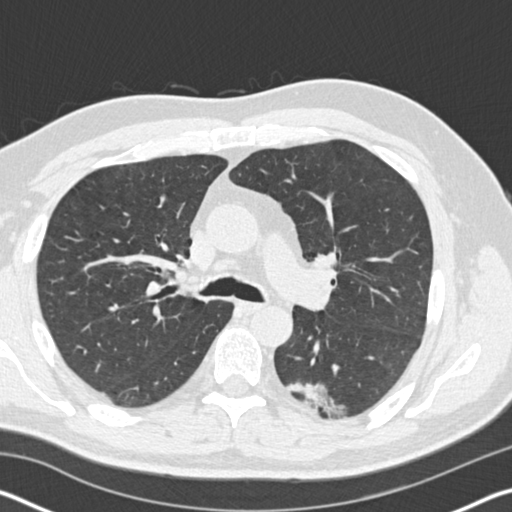
Axial slice from a low-dose chest CT screening exam, first (baseline) screen, lung window (W 1500 / L -600 HU), standard (soft-tissue) reconstruction kernel (B30f), 512 × 512 image matrix. Male, age 60 years at enrolment.
Expert-annotated lung lesion, bounding box (x1, y1, x2, y2) in pixels: (277, 364, 358, 425). The screening reader recorded 3 non-calcified nodules or masses ≥4 mm on this exam; which of them this box marks is not recorded. Participant outcome: lung cancer diagnosed 171 days after this screen — papillary adenocarcinoma, NOS, left lower lobe, moderately differentiated (G2), stage IB (AJCC 6th edition), 35 mm at pathology.